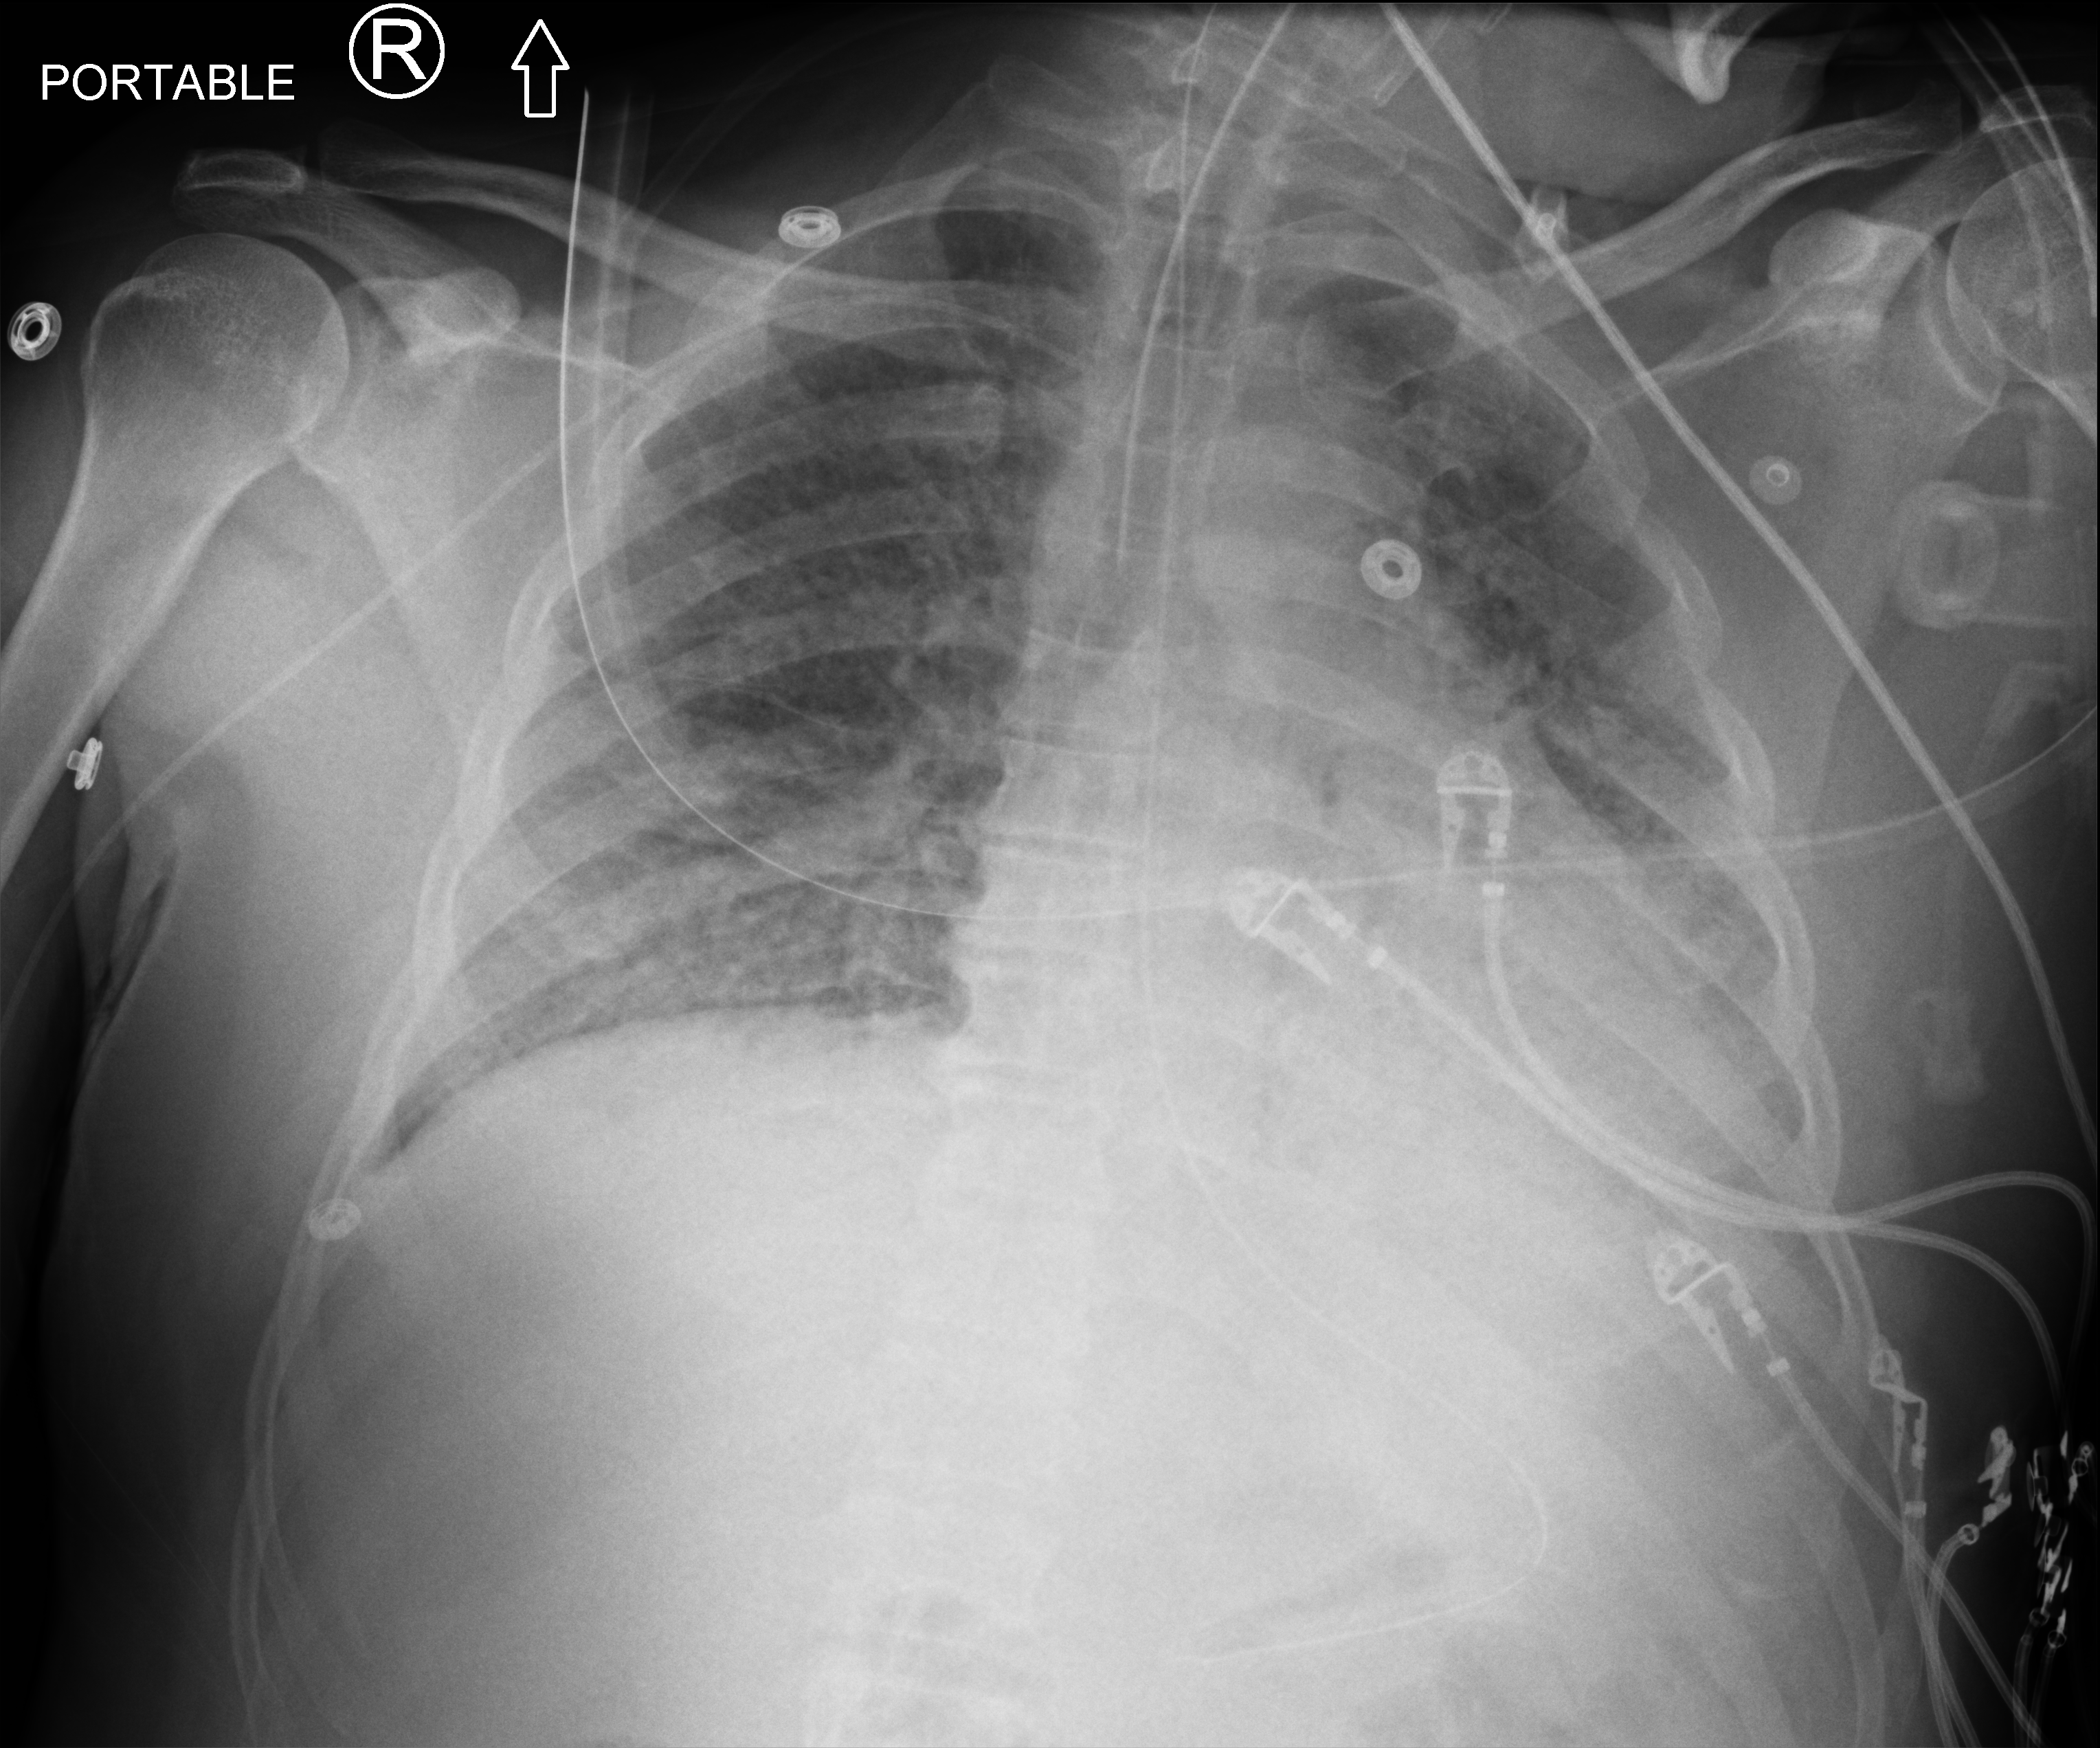
Portable chest radiograph; anteroposterior (AP) projection. Male patient hospitalised with COVID-19, age 18–59 years.
Admission-level facts for this patient (not findings on this image; timing relative to this image not recorded):
- admitted to intensive care during this hospital stay: yes
- chronic kidney disease (admission record): no